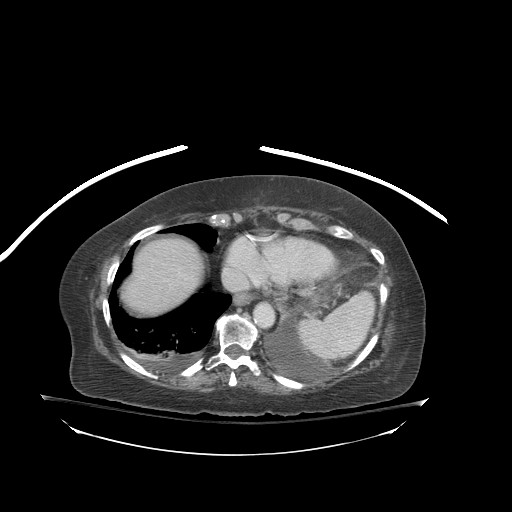
Contrast-enhanced abdominal CT (liver protocol), one axial slice. Position 76 of 81 along the scan axis. Reconstruction kernel STANDARD. Soft-tissue window (W 400 / L 40 HU). 512 × 512 image matrix. Case-level facts recorded for this patient, not image findings: diagnosis: hepatocellular carcinoma (patient treated with transarterial chemoembolisation; whether this scan precedes or follows treatment is not stated here); TNM stage (as recorded): Stage-I.
Structures marked on this image (semi-automatically segmented with operator editing):
- abdominal aorta: box from (x=255, y=303) to (x=273, y=326) px
- liver parenchyma outside the tumour (the mass and vessels are separate outlines, so this box may not span the whole liver): (x=123, y=238)–(x=202, y=314)